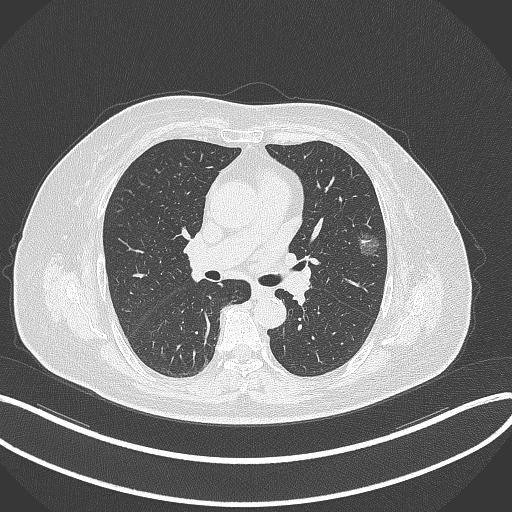
Chest CT, one axial slice. Slice 207 of 315 in the series (ordered by position). Reconstruction kernel B70f. 120 kVp. Lung window (W 1500 / L -600 HU). 512 × 512 image matrix, field of view 400 × 400 mm. Female patient, age 76 years. From the clinical record (not read from this slice): clinical TNM (as recorded): T1b N0 M0; histopathological grade: G1-2.
Structures marked on this image (rectangle marked by the reading radiologist):
- lung tumour (recorded histology: adenocarcinoma): bounding box [x1, y1, x2, y2] px = [353, 230, 383, 261]